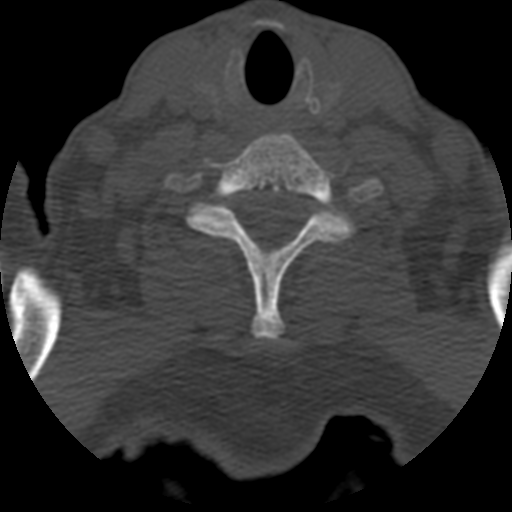
CT including the spine, one axial slice. Position 529 of 708 along the scan axis. Reconstruction kernel STANDARD. One of 3 acquisitions stored at this slice position. Bone window (W 1800 / L 400 HU). 1.25 mm slice thickness. 512 × 512 image matrix, field of view 160 × 160 mm. Patient age 55 years. From the clinical record (not read from this slice): primary cancer: colon; vertebrae with lytic lesions (as recorded): T12, L1, L5.
Outlined on this slice (semi-automatic segmentation, software-assisted and operator-edited):
- T1 vertebra: bounding box <184,201,359,237> (left, top, right, bottom; pixels)